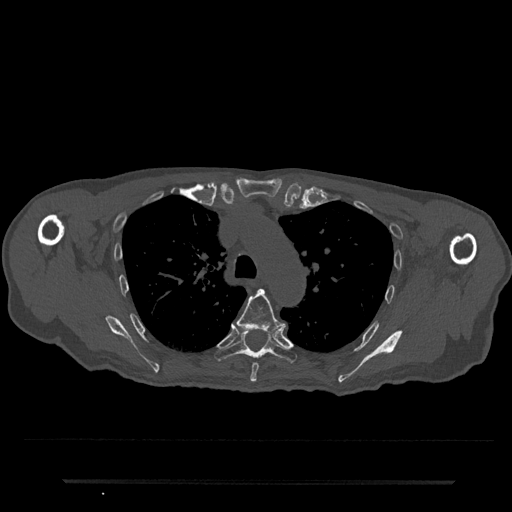
CT including the spine, one axial slice. Position 555 of 797 along the scan axis. 120 kVp. Bone window (W 1800 / L 400 HU). 0.5 mm slice thickness. 512 × 512 image matrix, field of view 427 × 427 mm. Male patient, age 74 years. From the clinical record (not read from this slice): primary cancer: prostate.
Structures marked on this image (semi-automatic segmentation, software-assisted and operator-edited):
- T5 vertebra: box from (x=236, y=289) to (x=286, y=382) px
- T6 vertebra: (x=214, y=329)–(x=297, y=363)